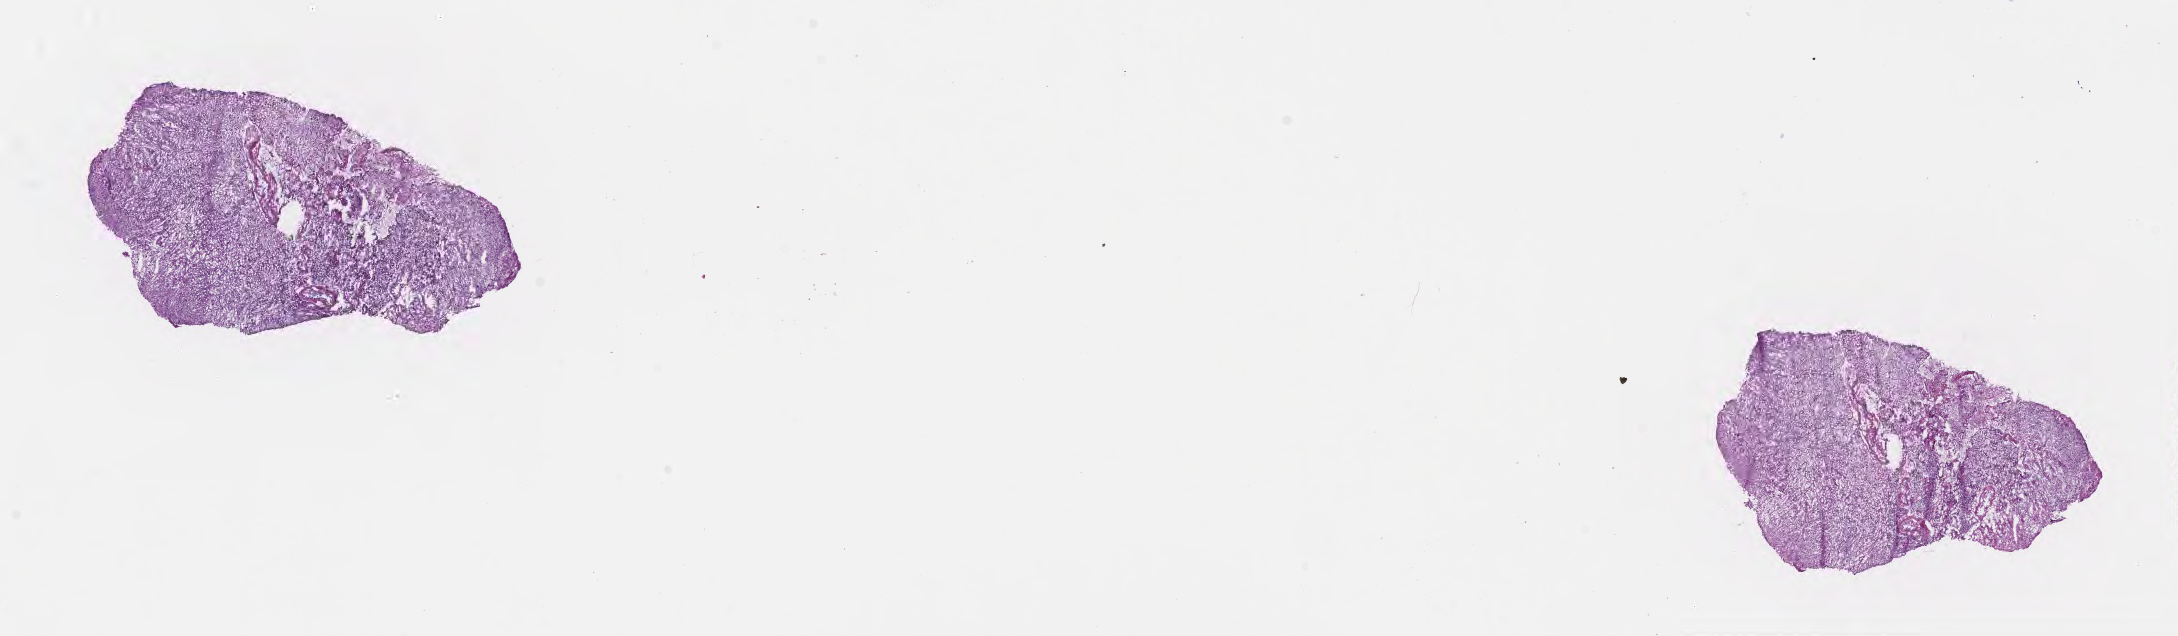
Haematoxylin and eosin whole-slide image, whole scanned area (about 17.6 x 5.1 mm) shown as a low-resolution overview. Frozen section (tissue freezing medium). Specimen: recurrent tumor. Anatomic site: brain. Male, age 49 years at initial diagnosis. Composition of this section per pathologist review: tumor cells 73%, tumor nuclei 82%, stromal cells 11%, necrosis 0%, normal cells 16%. Inflammatory infiltration, as recorded: lymphocyte infiltration 0%, monocyte infiltration 0%, neutrophil infiltration 0%.
- section: top of the tissue portion
- patient diagnosis: Glioblastoma, NOS